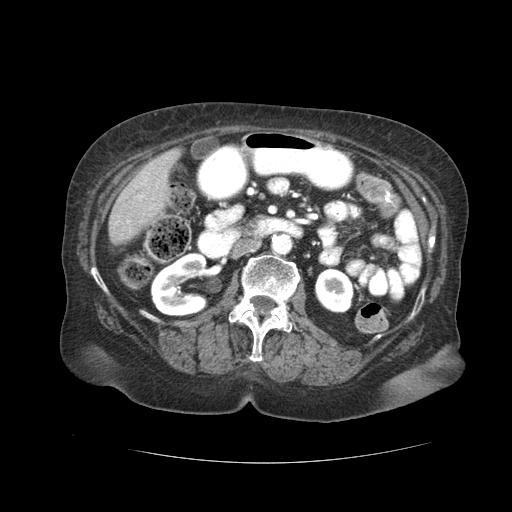
Contrast-enhanced abdominal CT (liver protocol), one axial slice; position 2 of 59 along the scan axis; soft-tissue window (W 400 / L 40 HU); 2.5 mm slice thickness; 512 × 512 image matrix, field of view 380 × 380 mm. Case-level facts recorded for this patient, not image findings: diagnosis: hepatocellular carcinoma (patient treated with transarterial chemoembolisation; whether this scan precedes or follows treatment is not stated here); TNM stage (as recorded): Stage-I; Child-Pugh class: A; tumour nodularity: uninodular.
Annotated regions visible in this slice (semi-automatically segmented with operator editing):
- liver parenchyma outside the tumour (the mass and vessels are separate outlines, so this box may not span the whole liver): box from (x=108, y=148) to (x=180, y=244) px